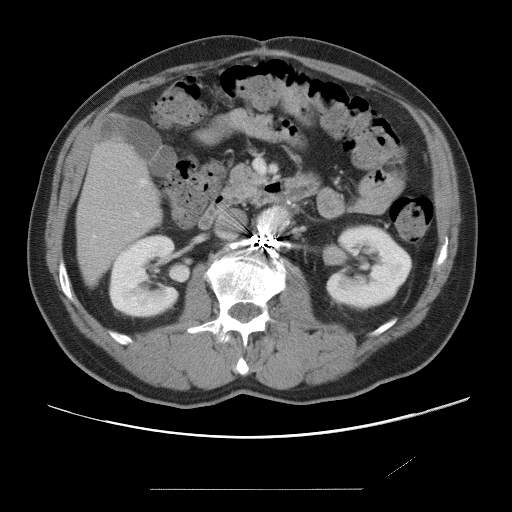
Contrast-enhanced abdominal CT, one axial slice; position 24 of 87 along the scan axis; 120 kVp; intravenous contrast given; soft-tissue window (W 400 / L 40 HU); 5 mm slice thickness; 512 × 512 image matrix, field of view 406 × 406 mm. Male patient, age 74 years. Case-level facts recorded for this patient, not image findings: diagnosis: colorectal cancer liver metastases, imaged before liver resection; multiple liver metastases: yes; largest metastasis: 1.1 cm.
Annotated regions visible in this slice (expert manual segmentation):
- hepatic veins: bounding box [x1, y1, x2, y2] px = [93, 179, 146, 238]
- liver: [77, 143, 157, 281]
- planned liver remnant (the part of the liver to remain after resection): [77, 143, 157, 281]
- portal vein (with intrahepatic branches): [135, 213, 139, 216]